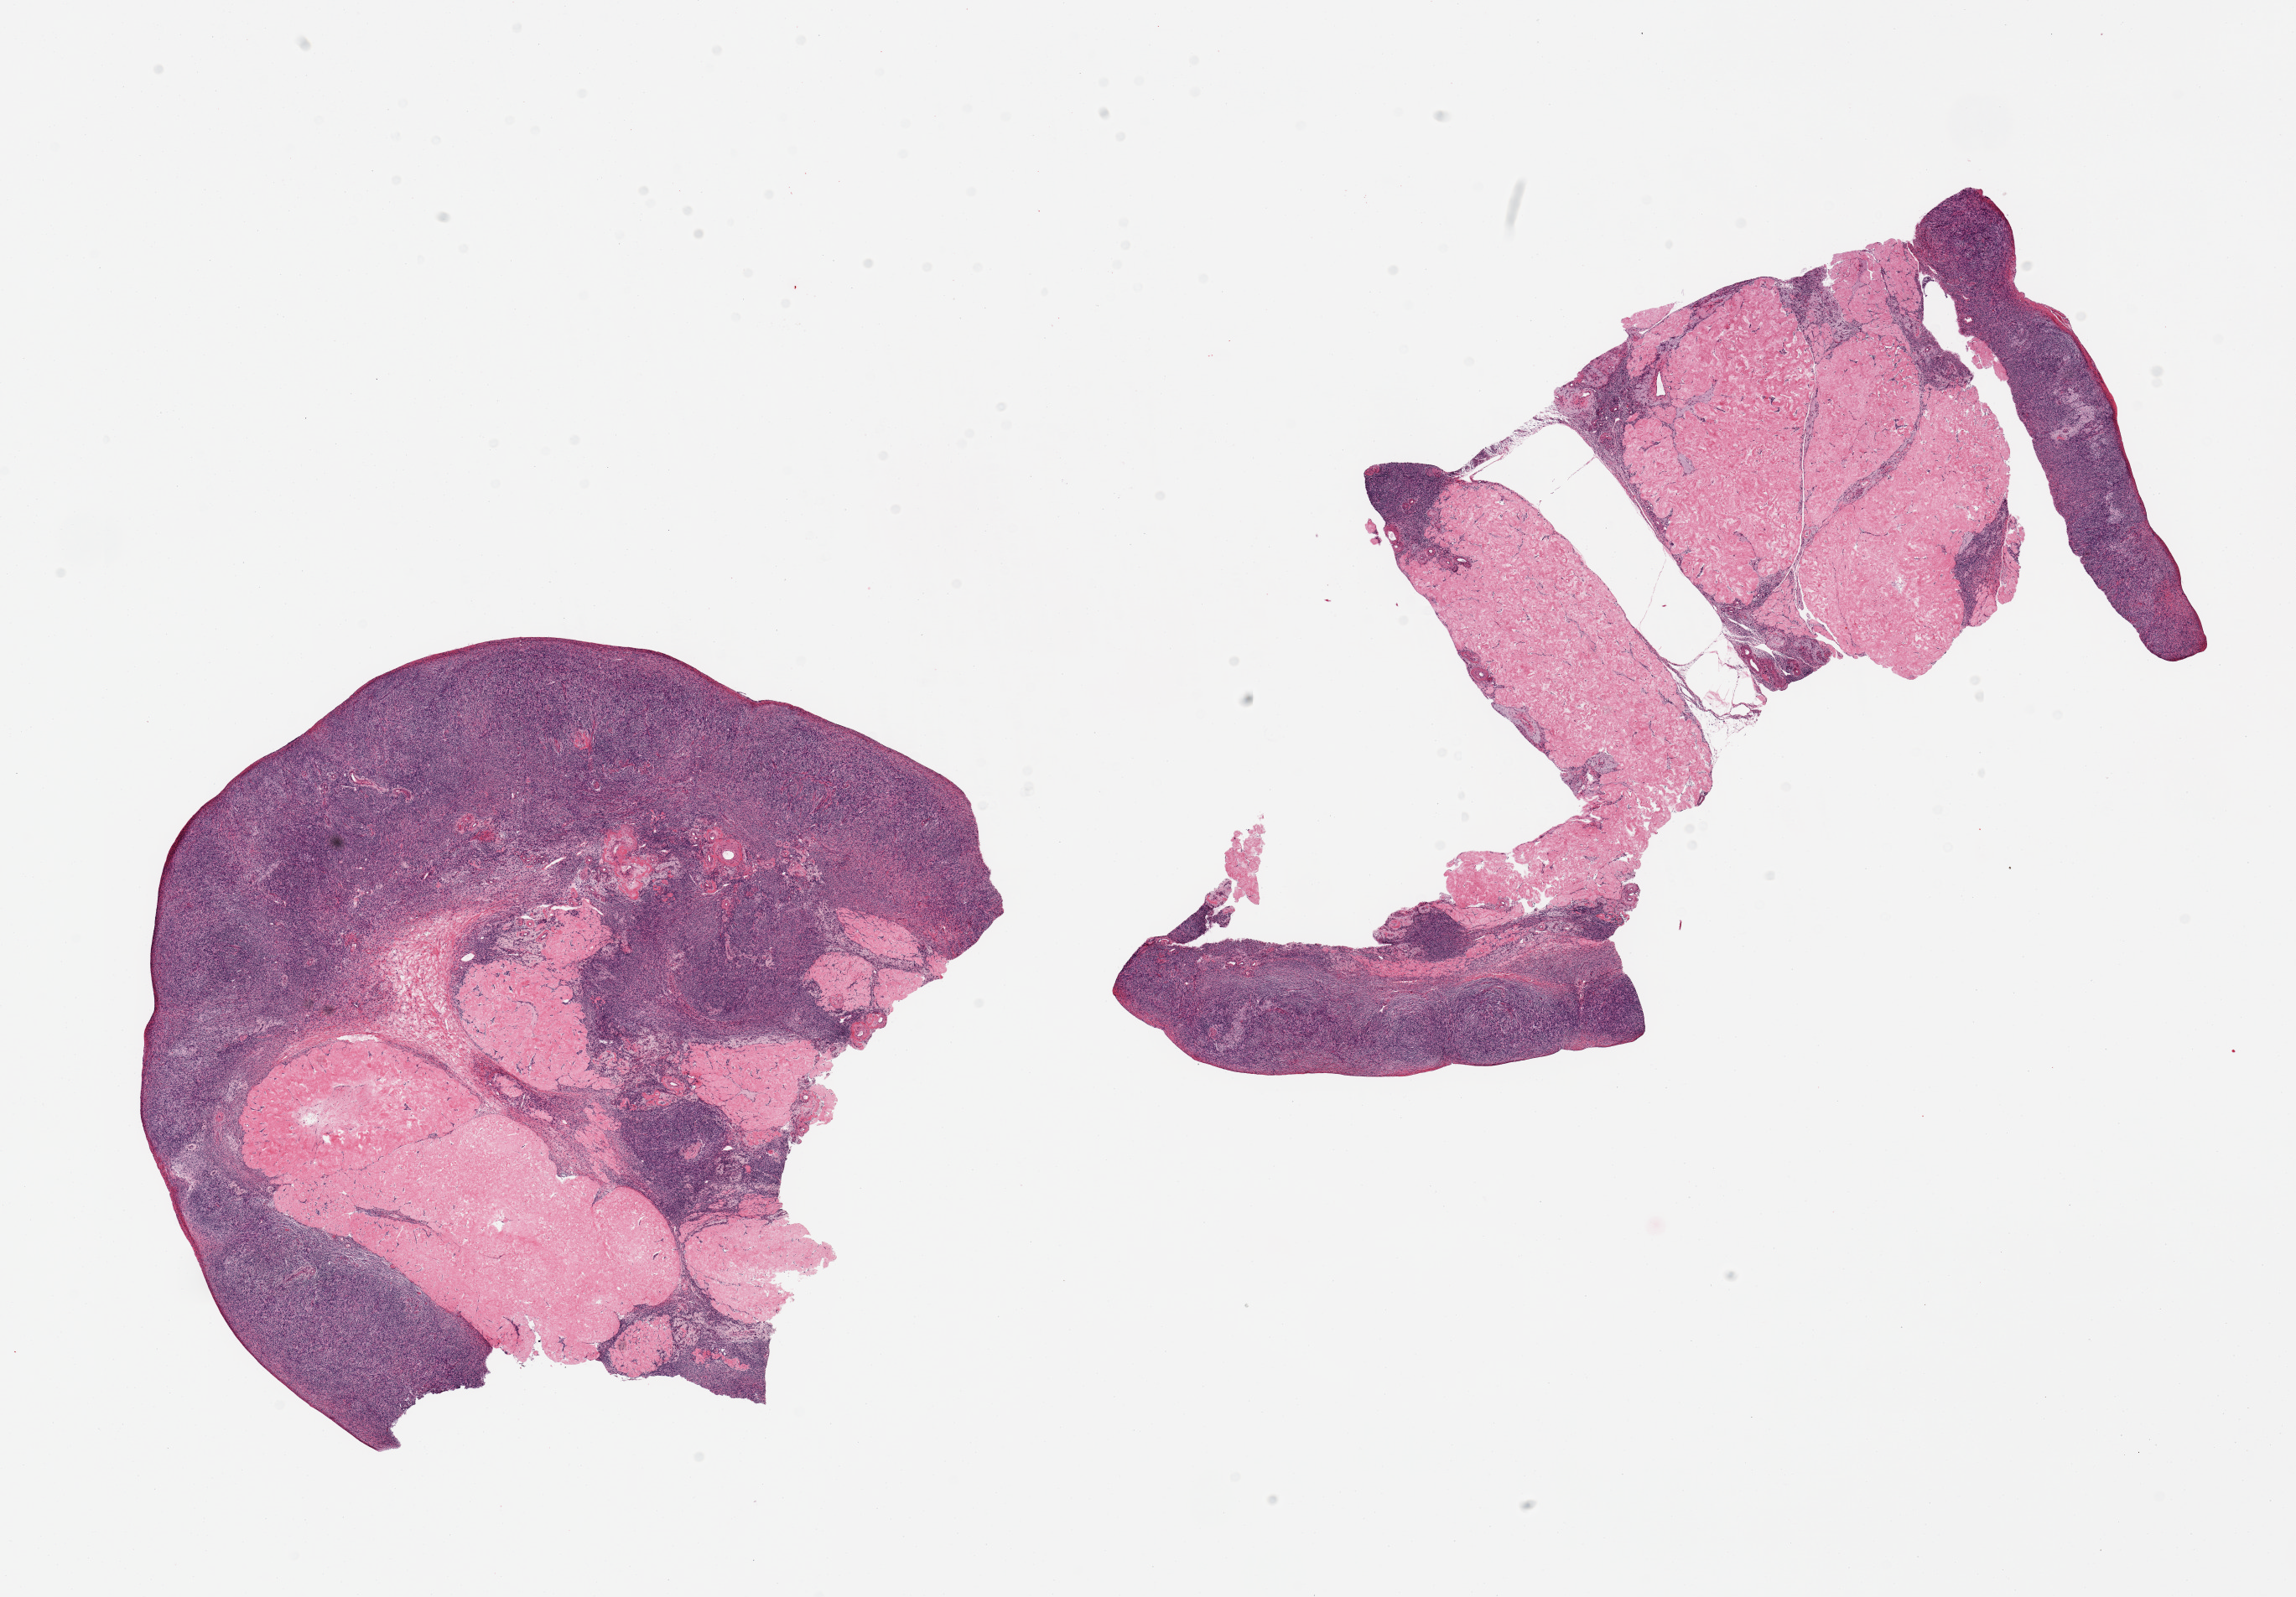
Digitized haematoxylin and eosin-stained section, shown as a low-resolution overview of the whole scanned area (about 21.7 x 15.1 mm), PAXgene-fixed paraffin-embedded (PFPE) section, section of ovary (target tissue), tissue donor sample. Donor sex: female.
Reviewer comment on this tissue sample: 2 fragmented pieces; atrophic with large corpora amylacia (>50%).